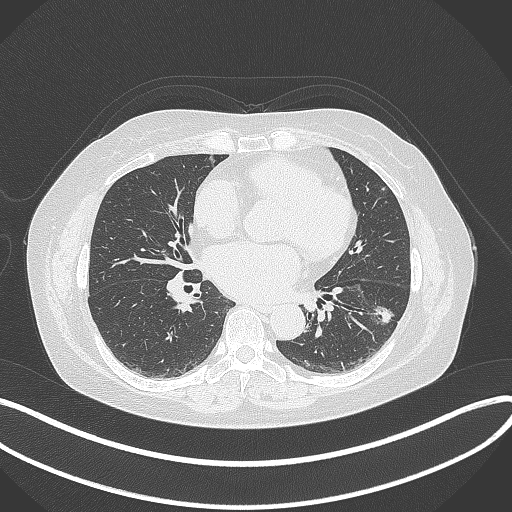
Chest CT, one axial slice. Position 165 of 373 along the scan axis. Reconstruction kernel B70f. 120 kVp. Lung window (W 1500 / L -600 HU). 1 mm slice thickness. 512 × 512 image matrix, field of view 400 × 400 mm. Female patient, age 67 years. From the clinical record (not read from this slice): clinical TNM (as recorded): T1c N0 M0; histopathological grade: G2.
Annotated regions visible in this slice (rectangle marked by the reading radiologist):
- lung tumour (recorded histology: adenocarcinoma): box from (x=366, y=302) to (x=399, y=327) px